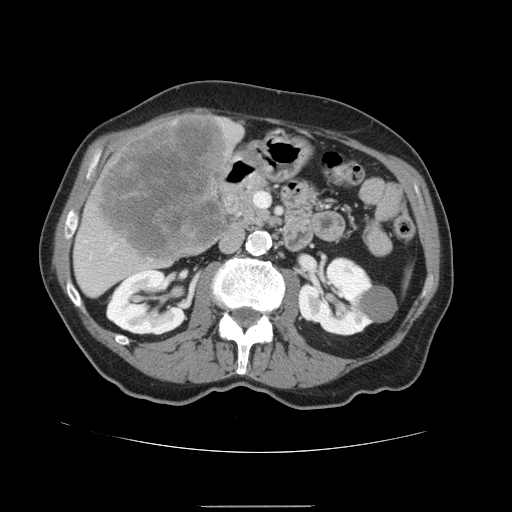
Contrast-enhanced abdominal CT, one axial slice. Position 62 of 168 along the scan axis. Intravenous contrast given. Soft-tissue window (W 400 / L 40 HU). 512 × 512 image matrix. Male patient, age 74 years. Case-level facts recorded for this patient, not image findings: diagnosis: colorectal cancer liver metastases, imaged before liver resection; multiple liver metastases: no; largest metastasis: 14.5 cm; disease in both lobes: yes.
Annotated regions visible in this slice (manually delineated by an expert):
- liver: bounding box [x1, y1, x2, y2] px = [73, 114, 244, 298]
- liver metastasis: [98, 118, 227, 260]